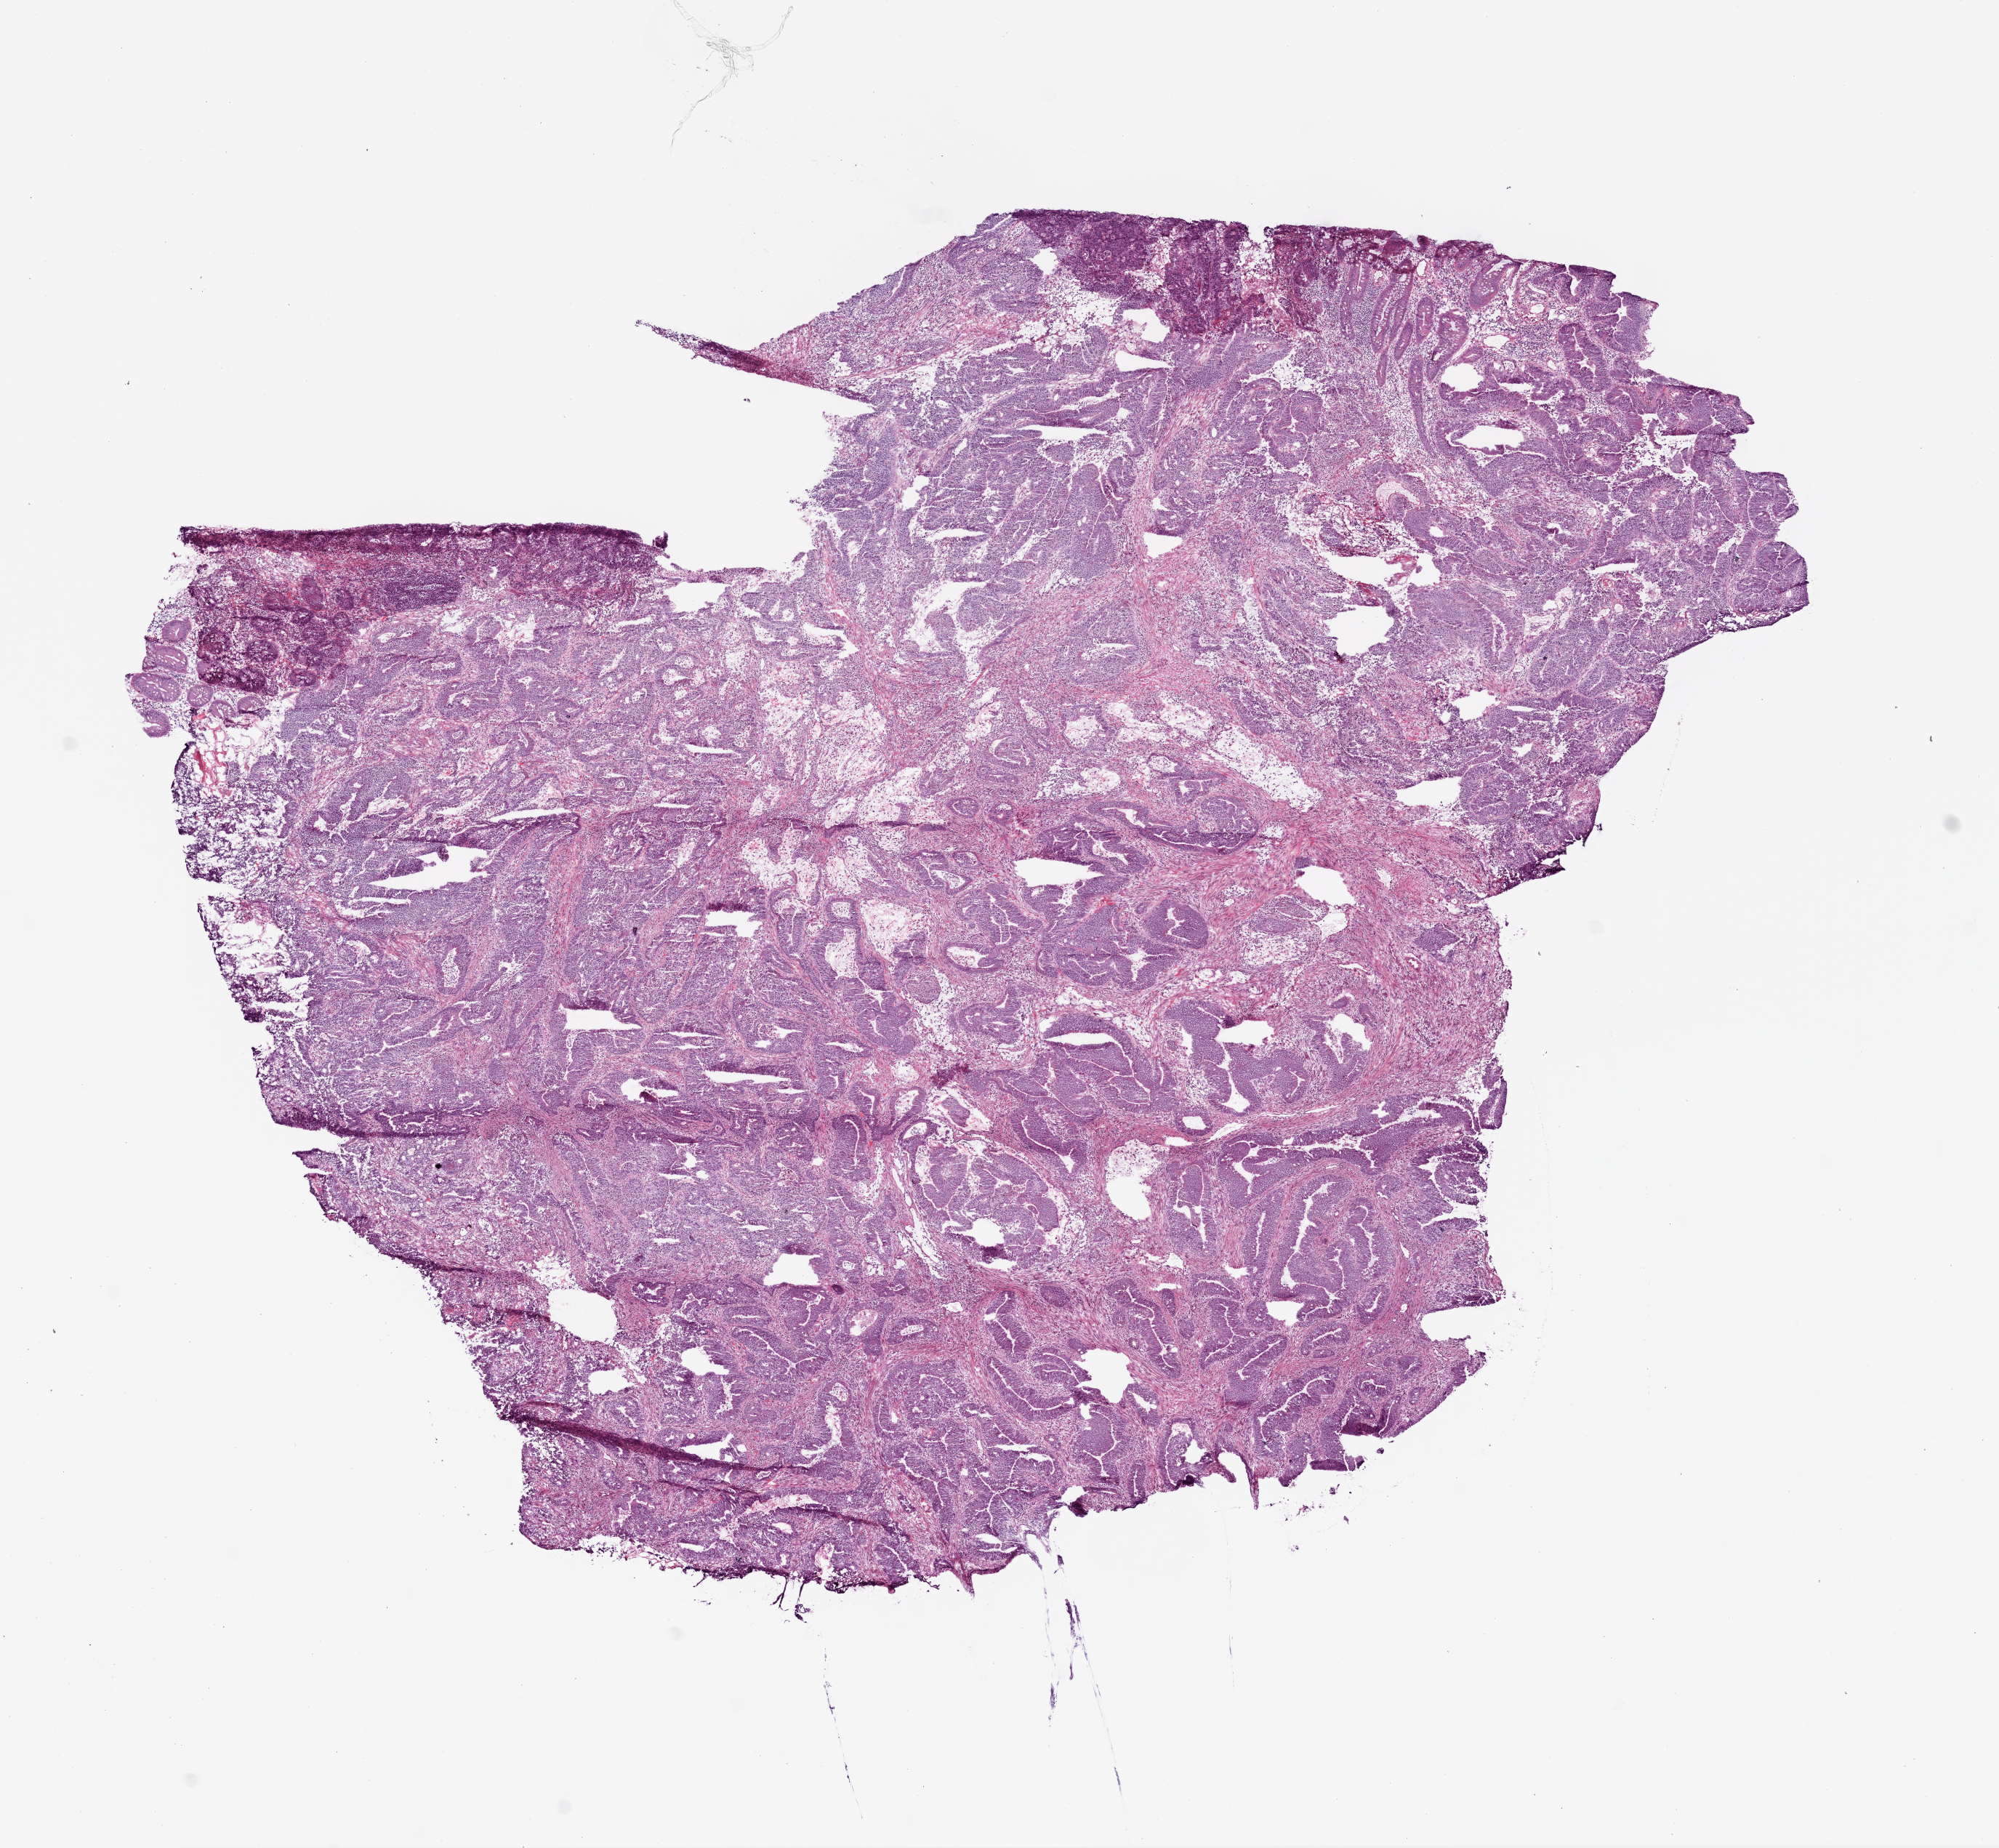
Digitized H&E-stained tissue section (whole slide) — whole scanned area (about 11.0 x 10.2 mm, from a 20x scan) shown as a low-resolution overview; frozen section; primary tumour sample from the colon. Male, age 57 years at initial diagnosis. Pathologist review of this section (percent, as recorded): tumour cells 80%, tumour nuclei 90%, normal cells 5%, stromal cells 15%, necrosis 0%. Infiltration values recorded for this section: lymphocyte infiltration 5%.
* lymph nodes positive (case pathology): 0 of 17 examined
* AJCC pathologic stage: I
* diagnosis: Adenocarcinoma, NOS
* TNM: T2 N0 M0